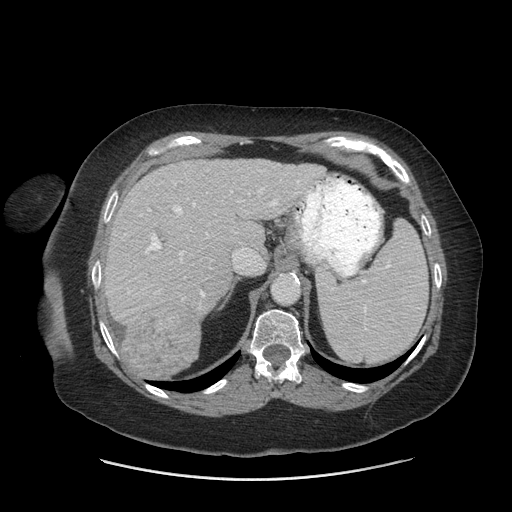
Contrast-enhanced abdominal CT (liver protocol), one axial slice; position 49 of 69 along the scan axis; reconstruction kernel STANDARD; 140 kVp; soft-tissue window (W 400 / L 40 HU); 512 × 512 image matrix, field of view 420 × 420 mm. From the clinical record (not read from this slice): diagnosis: hepatocellular carcinoma (patient treated with transarterial chemoembolisation; whether this scan precedes or follows treatment is not stated here); TNM stage (as recorded): Stage-IIIB; Child-Pugh class: A; tumour differentiation: moderately differentiated.
Structures marked on this image (semi-automatic segmentation, software-assisted and operator-edited):
- liver parenchyma outside the tumour (the mass and vessels are separate outlines, so this box may not span the whole liver): bounding box <102,158,324,347> (left, top, right, bottom; pixels)
- mass: <122,302,199,379>
- liver vessels: <125,170,300,297>